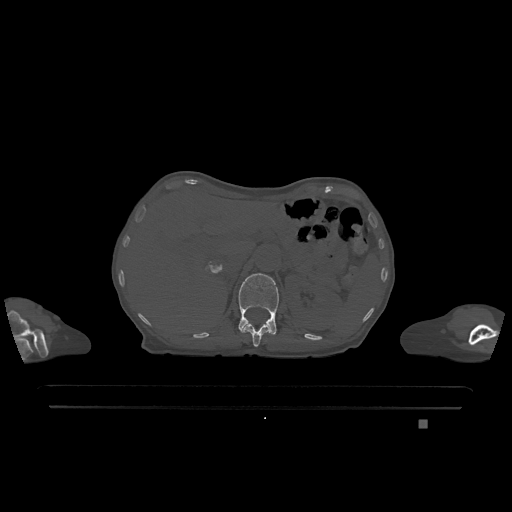
CT including the spine, one axial slice; slice 498 of 1317 in the series (ordered by position); bone window (W 1800 / L 400 HU); 0.5 mm slice thickness; 512 × 512 image matrix, field of view 500 × 500 mm. Patient: female, 74 years. From the clinical record (not read from this slice): primary cancer: lung; vertebrae with lytic lesions (as recorded): T1, T4, T5, T6, L4, L5.
Outlined on this slice (semi-automatic segmentation, software-assisted and operator-edited):
- L1 vertebra: bounding box [x1, y1, x2, y2] px = [238, 273, 279, 335]
- T12 vertebra: [242, 318, 270, 347]